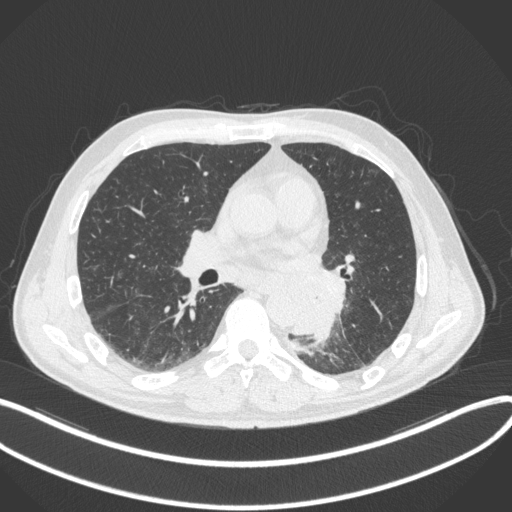
Chest CT, one axial slice; reconstruction kernel B31f; 120 kVp; lung window (W 1500 / L -600 HU); 1 mm slice thickness; 512 × 512 image matrix, field of view 400 × 400 mm. Patient: male, 59 years. From the clinical record (not read from this slice): clinical TNM (as recorded): T2a N2 M0.
Outlined on this slice (rectangle marked by the reading radiologist):
- lung tumour (recorded histology: squamous cell carcinoma): bounding box (x1, y1, x2, y2) in pixels: (286, 270, 350, 347)